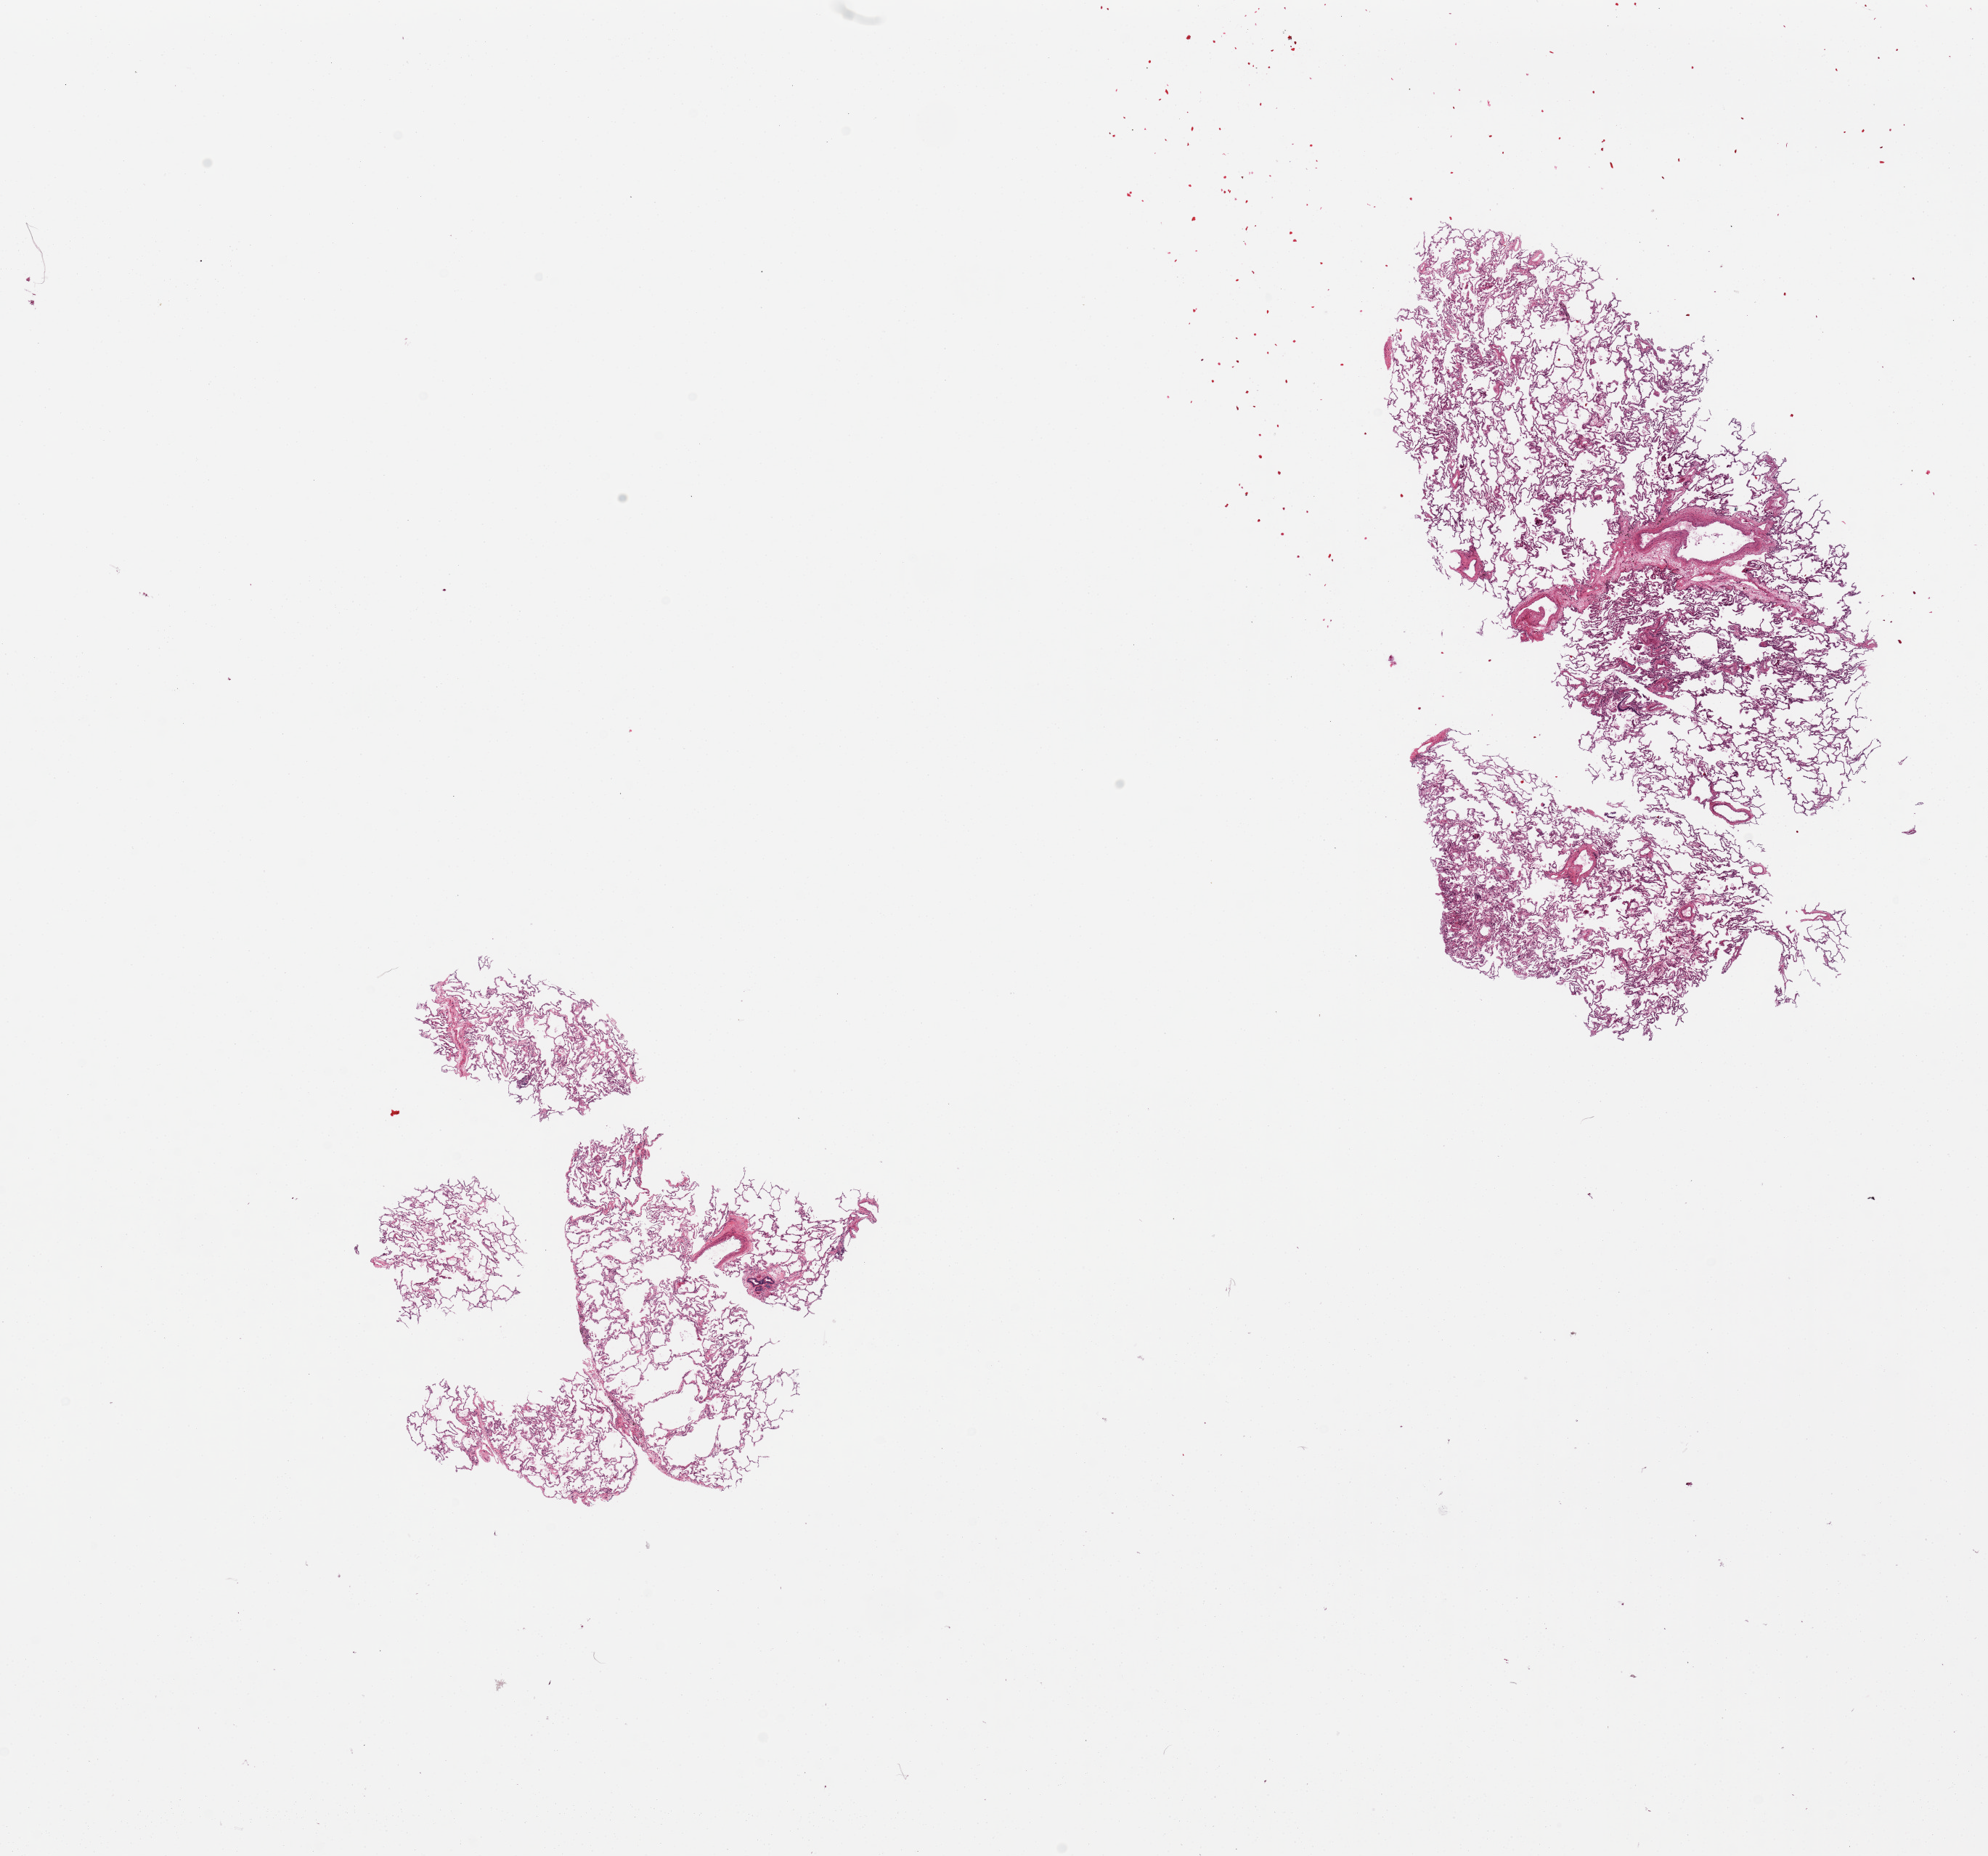
Whole-slide image, H&E stain, brightfield, shown as a low-resolution overview of the whole scanned area (about 21.7 x 20.2 mm); PAXgene-fixed, paraffin-embedded tissue; section of lung (target tissue); donor tissue sample. Male donor.
Review note (as recorded): 2 small, irregular, fragmented pieces (7x5 & 5x5mm).